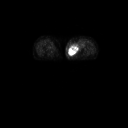
FDG PET of an extremity soft-tissue mass (from a PET/CT study), one axial slice. Position 19 of 91 along the scan axis. 3.27 mm slice thickness. 128 × 128 image matrix, field of view 700 × 700 mm. Female patient, age 74 years. Case-level facts recorded for this patient, not image findings: histological type: pleomorphic leiomyosarcoma; grade: high; site of the primary tumour: left thigh.
Structures marked on this image (expert contour drawn on MRI and transferred to this co-registered scan by the dataset authors):
- gross tumour volume including surrounding oedema: bounding box (x1, y1, x2, y2) in pixels: (68, 41, 85, 55)
- gross tumour volume (mass): (68, 46, 79, 55)